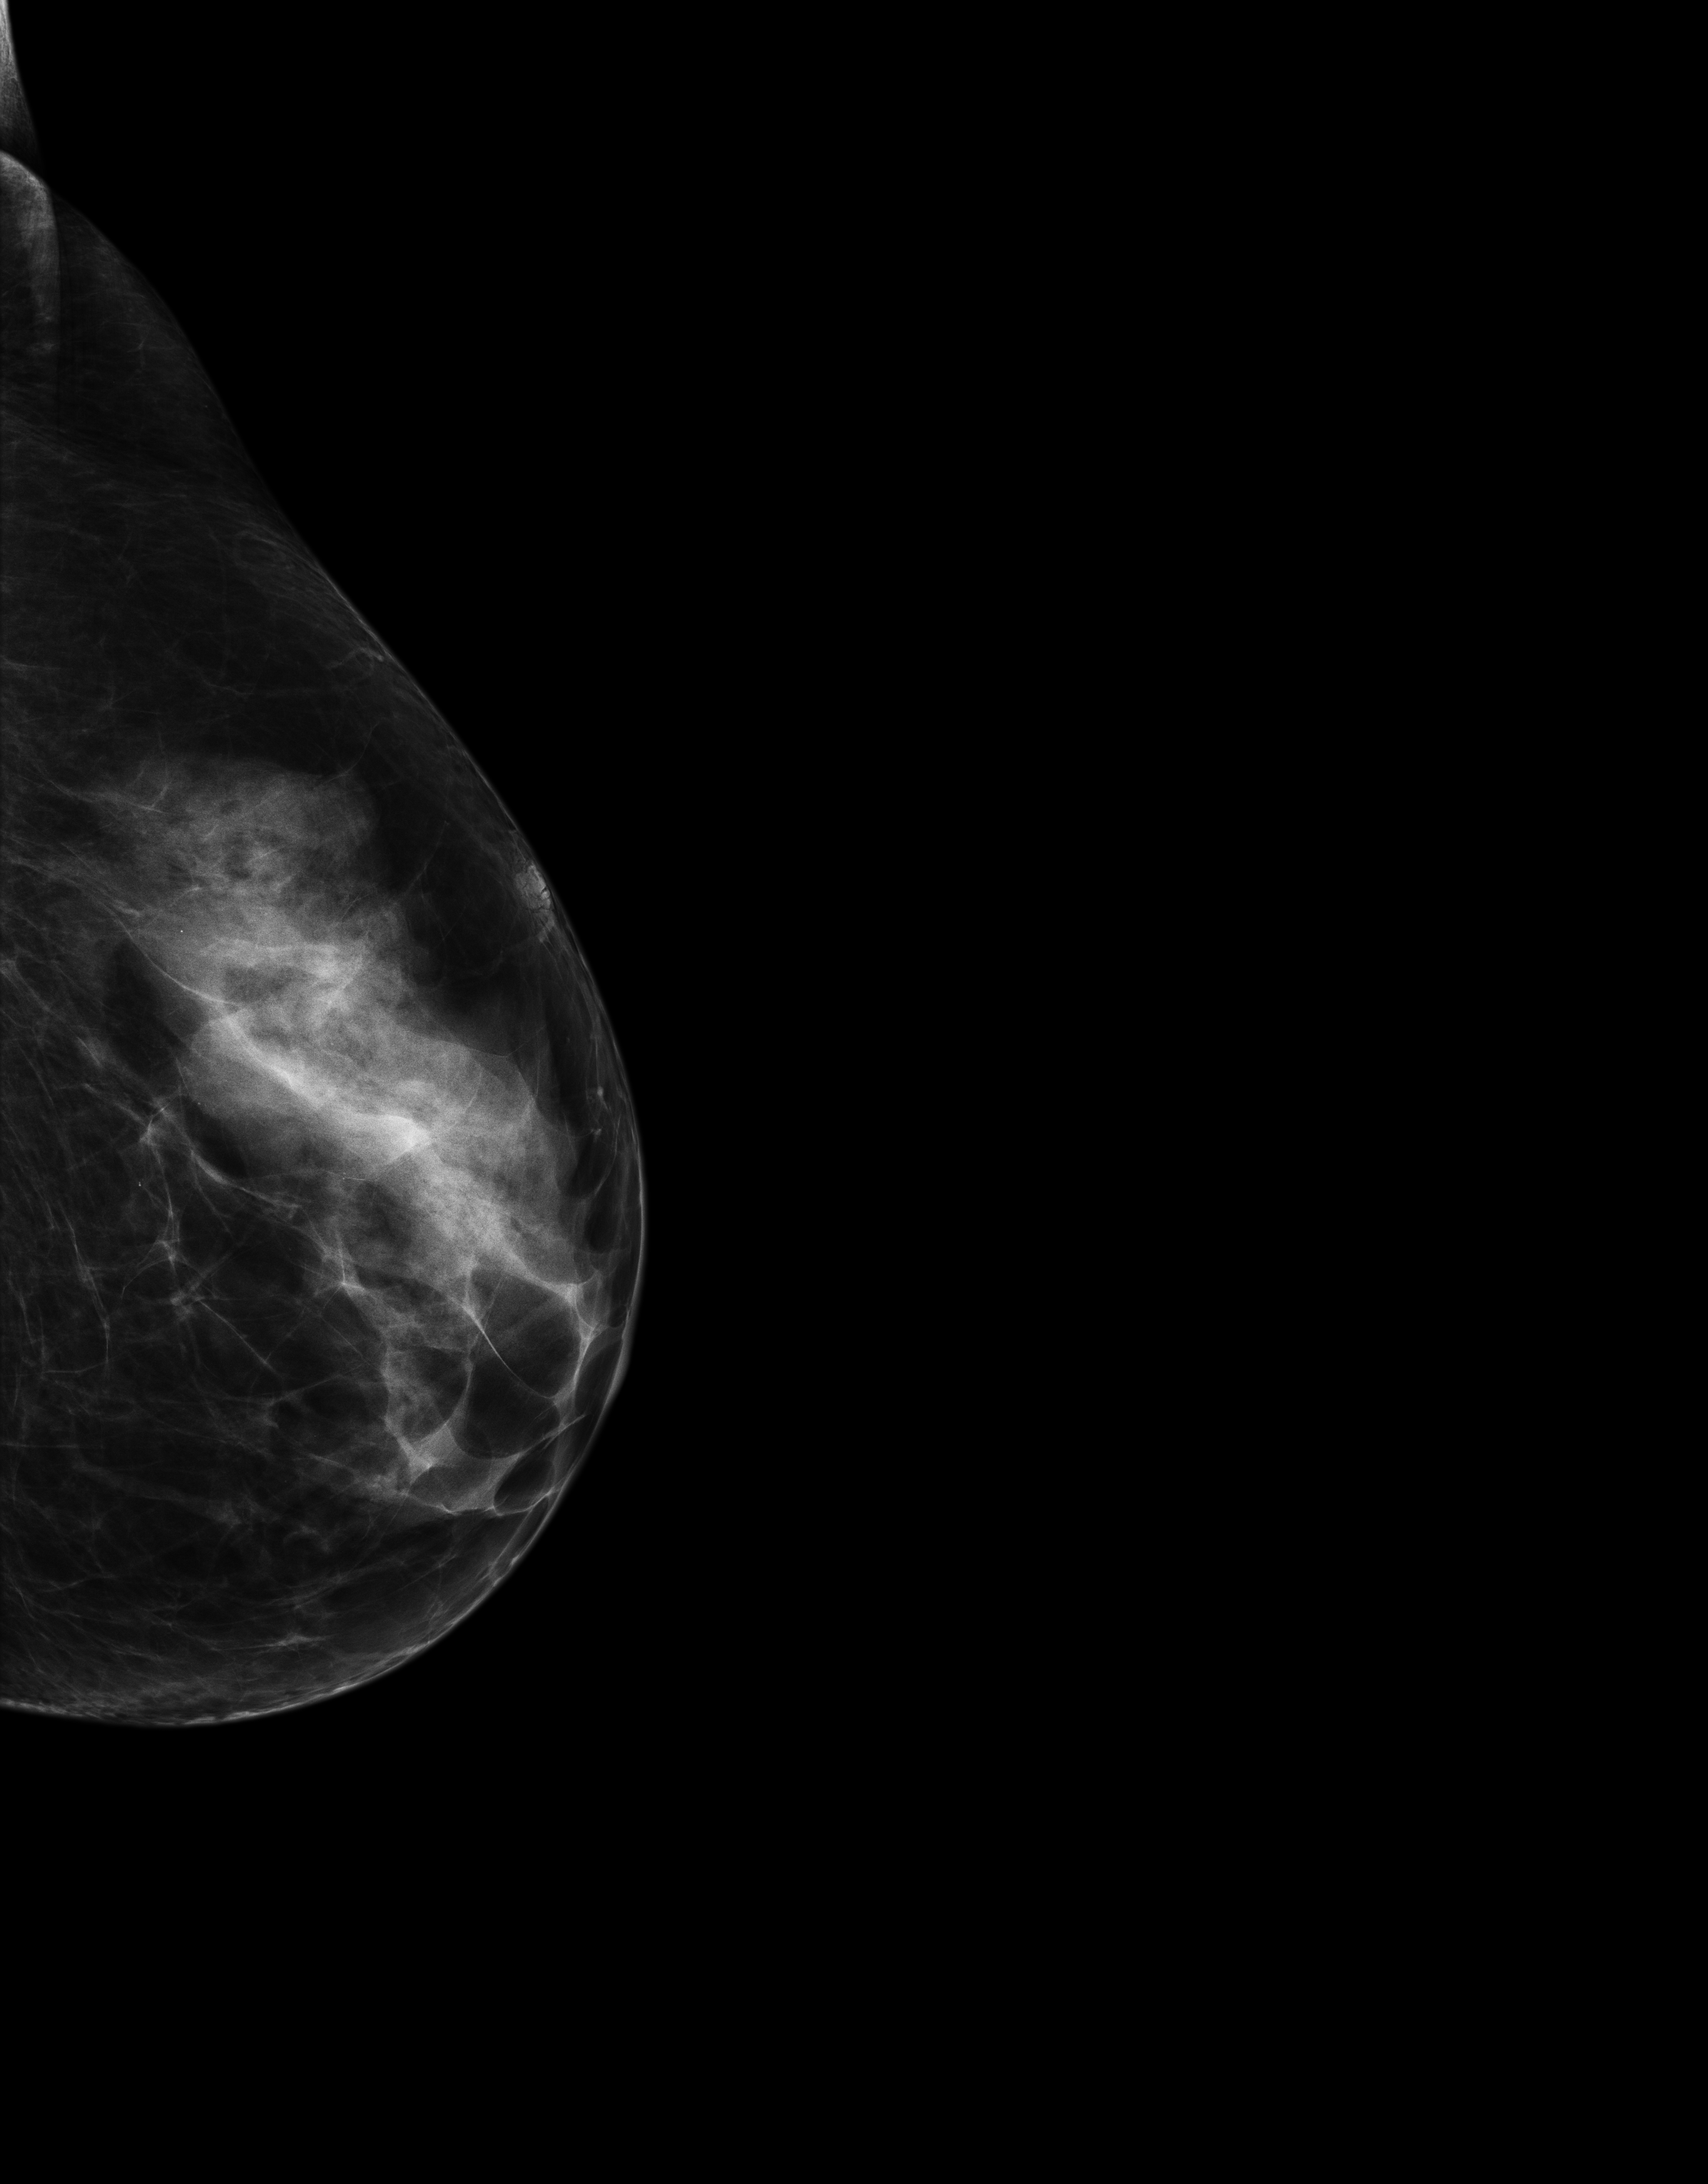
Full-field digital mammogram (FFDM); left breast; exaggerated CC view (lateral); annual screening mammography examination; system: Senographe Essential ADS_56.21.3. Patient: female, 51 years.
- BI-RADS breast density category at the screening exam (both breasts, scale 1–4): 3
- final BI-RADS category for the screening round (tomosynthesis exam, both breasts): category 1
- recall: no recall after this screen